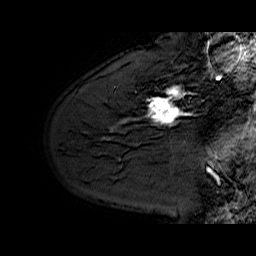
Breast MRI (dynamic contrast-enhanced), one sagittal slice; position 46 of 60 along the scan axis; dynamic contrast-enhanced series, time point 2 of 6 at this slice position (early post-contrast); 1.5 T; TE 6.4 ms, TR 32.9 ms; 4 mm slice thickness; 256 × 256 image matrix. Female patient. Case-level facts recorded for this patient, not image findings: setting: breast cancer imaged before/during neoadjuvant chemotherapy; receptor status: HER2-positive.
Outlined on this slice (semi-automatically segmented with operator editing):
- analysis volume of interest (the breast-tissue region the enhancement analysis was run in; not a lesion): bounding box [x1, y1, x2, y2] px = [130, 62, 210, 128]
- tumour enhancement mask (voxels above the 100 % enhancement threshold inside the analysis volume of interest): [149, 86, 181, 125]